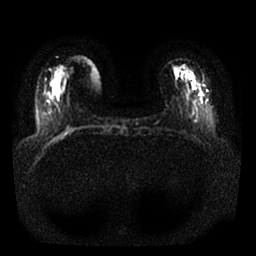
Breast MRI, one axial slice; diffusion-weighted series; image 2 of 4 stored at this slice position (different b-values; order by instance number); 1.5 T; 256 × 256 image matrix, field of view 330 × 330 mm. Female patient.
Annotated regions visible in this slice (outlined manually by an expert reader):
- tumour on diffusion-weighted imaging: box from (x=200, y=94) to (x=203, y=96) px